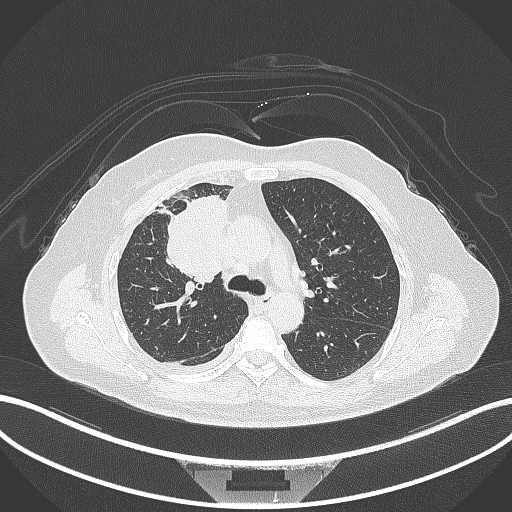
Chest CT, one axial slice; slice 188 of 305 in the series (ordered by position); reconstruction kernel B70f; 120 kVp; lung window (W 1500 / L -600 HU); 1 mm slice thickness; 512 × 512 image matrix, field of view 400 × 400 mm. Patient: female, 52 years. From the clinical record (not read from this slice): clinical TNM (as recorded): T3 N1 M1.
Annotated regions visible in this slice (bounding box drawn by a radiologist):
- lung tumour (recorded histology: adenocarcinoma): box from (x=160, y=195) to (x=232, y=289) px